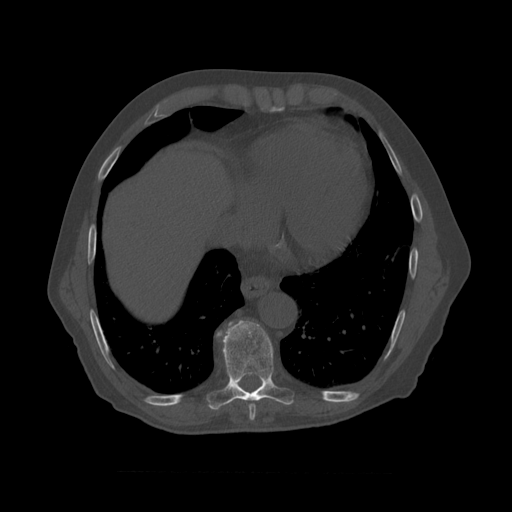
CT including the spine, one axial slice; slice 447 of 450 in the series (ordered by position); reconstruction kernel STANDARD; 120 kVp; bone window (W 1800 / L 400 HU); 1.25 mm slice thickness; 512 × 512 image matrix, field of view 405 × 405 mm. Patient age 75 years. From the clinical record (not read from this slice): primary cancer: prostate.
Structures marked on this image (semi-automatic segmentation, software-assisted and operator-edited):
- T8 vertebra: box from (x=216, y=320) to (x=294, y=411) px